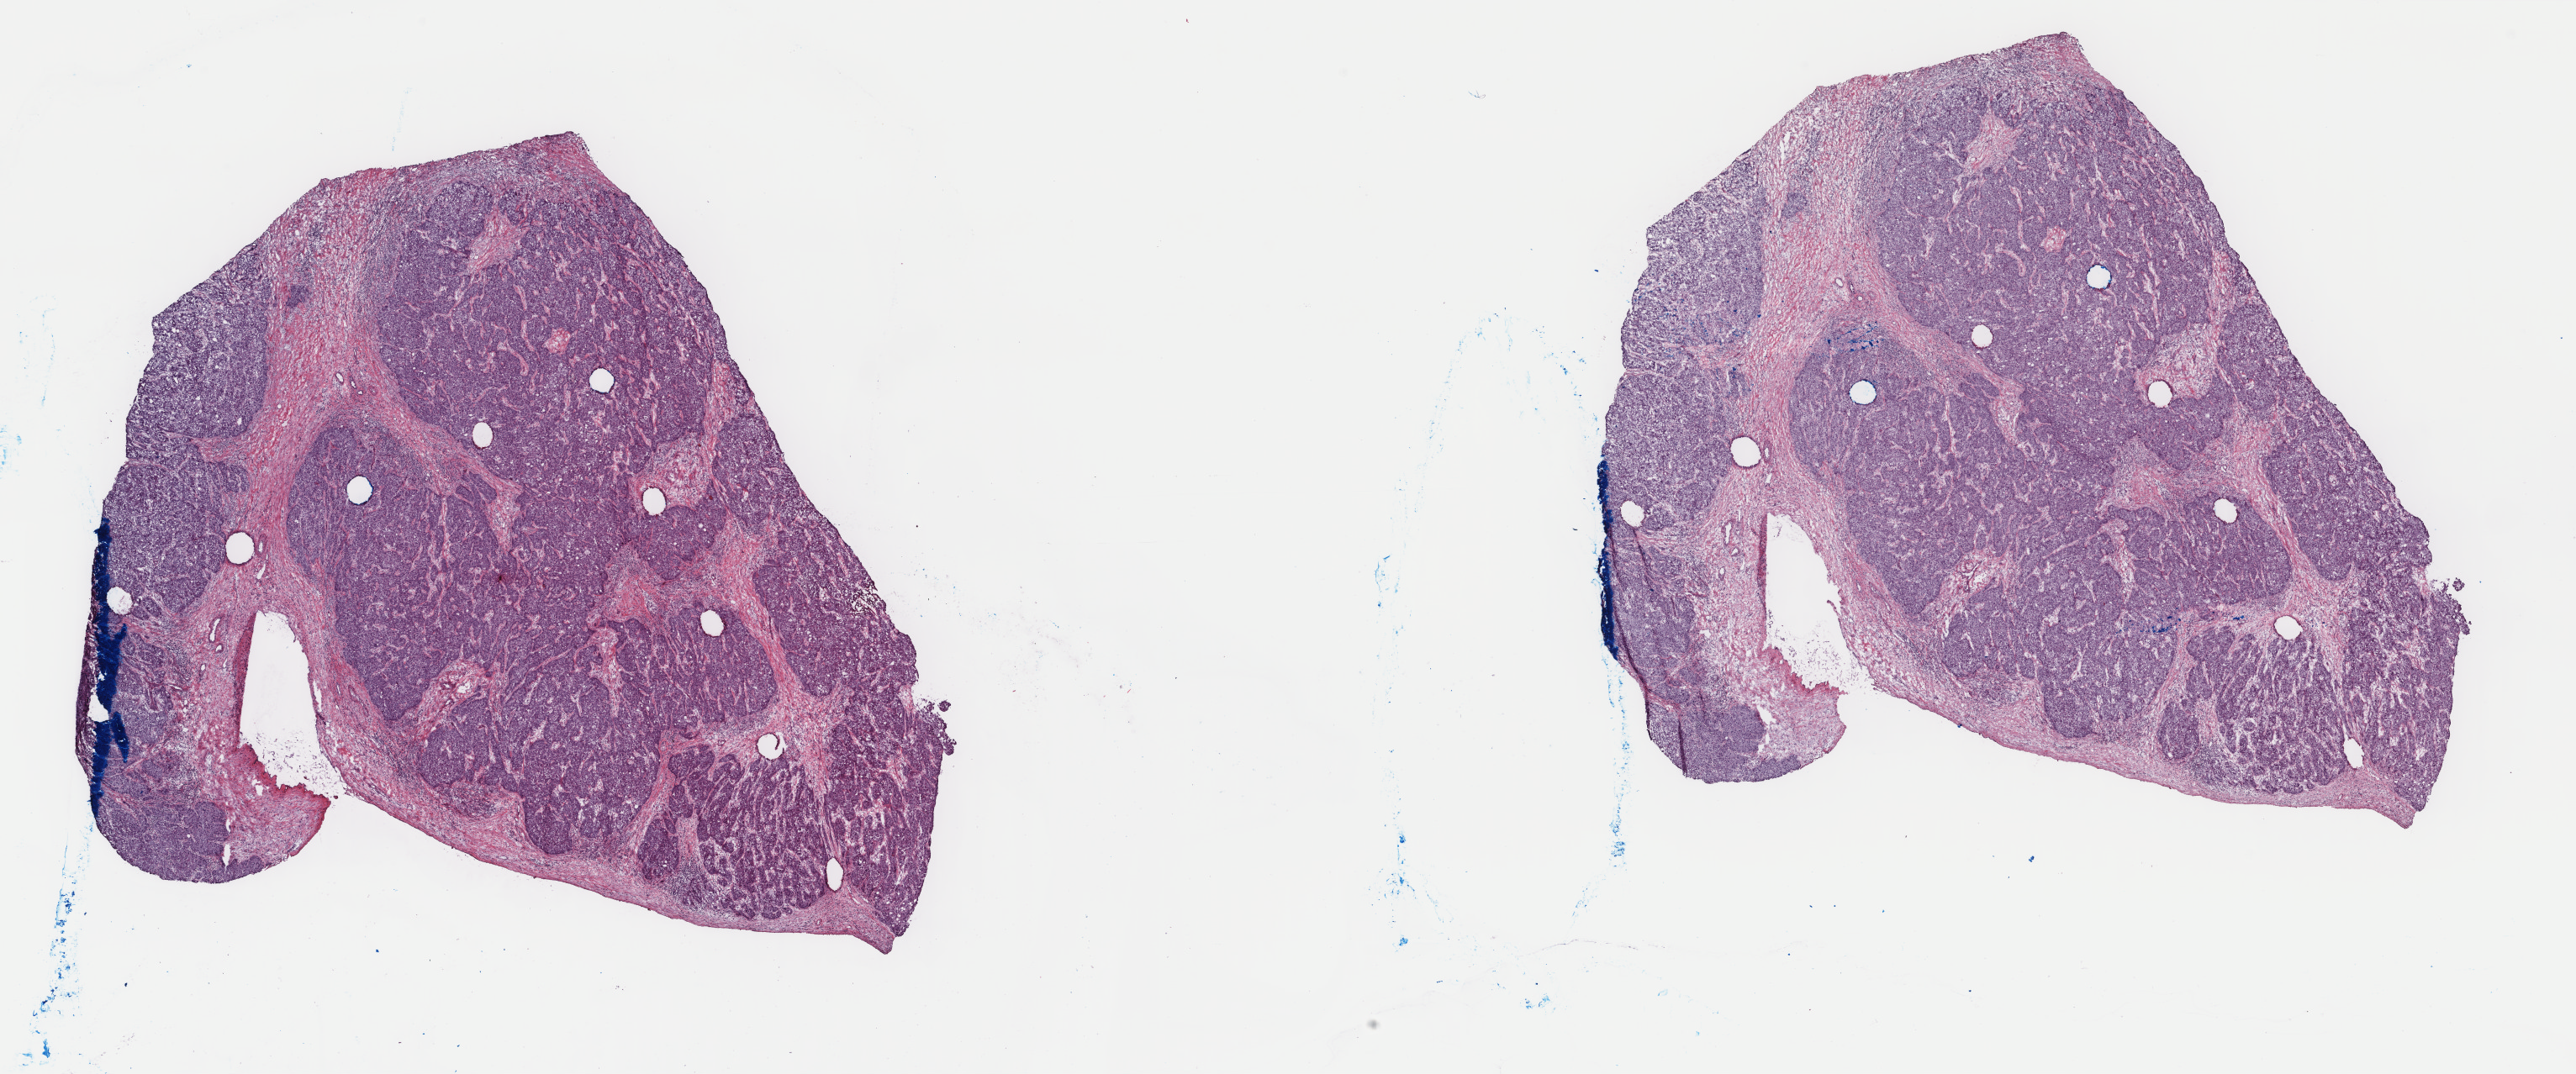
Hematoxylin and eosin (H&E) stained whole-slide image, a low-resolution overview of the entire scanned area, about 24.3 x 10.1 mm (acquisition: 40x scan); frozen section from the top of the tissue portion; primary tumour sample from the liver. Female patient; age at initial diagnosis 81 years. Histologic grade: G2 (moderately differentiated). Pathologist review of this section (percent, as recorded): tumour cells 100%, tumour nuclei 80%, normal cells 0%, stromal cells 0%, necrosis 0%. Infiltration values recorded for this section: lymphocyte infiltration 5%, monocyte infiltration 0%, neutrophil infiltration 0%.
AJCC pathologic stage: II (7th edition). Diagnosis: Hepatocellular carcinoma, NOS.